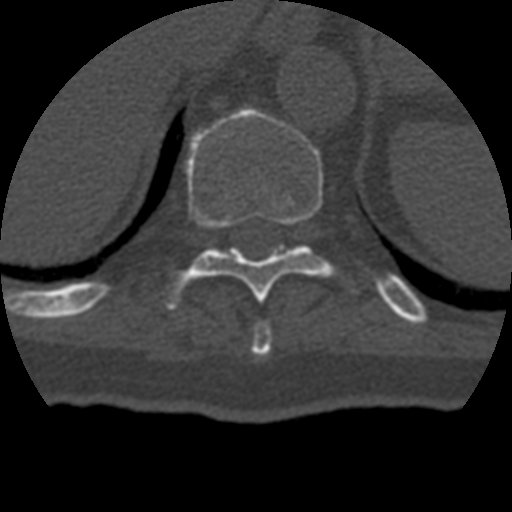
CT including the spine, one axial slice; position 216 of 399 along the scan axis; reconstruction kernel STANDARD; 120 kVp; bone window (W 1800 / L 400 HU); 1.25 mm slice thickness; 512 × 512 image matrix, field of view 160 × 160 mm. Patient age 69 years. From the clinical record (not read from this slice): primary cancer: prostate.
Outlined on this slice (semi-automatically segmented with operator editing):
- T10 vertebra: box from (x=167, y=108) to (x=334, y=308) px
- T9 vertebra: (x=252, y=322)–(x=272, y=356)